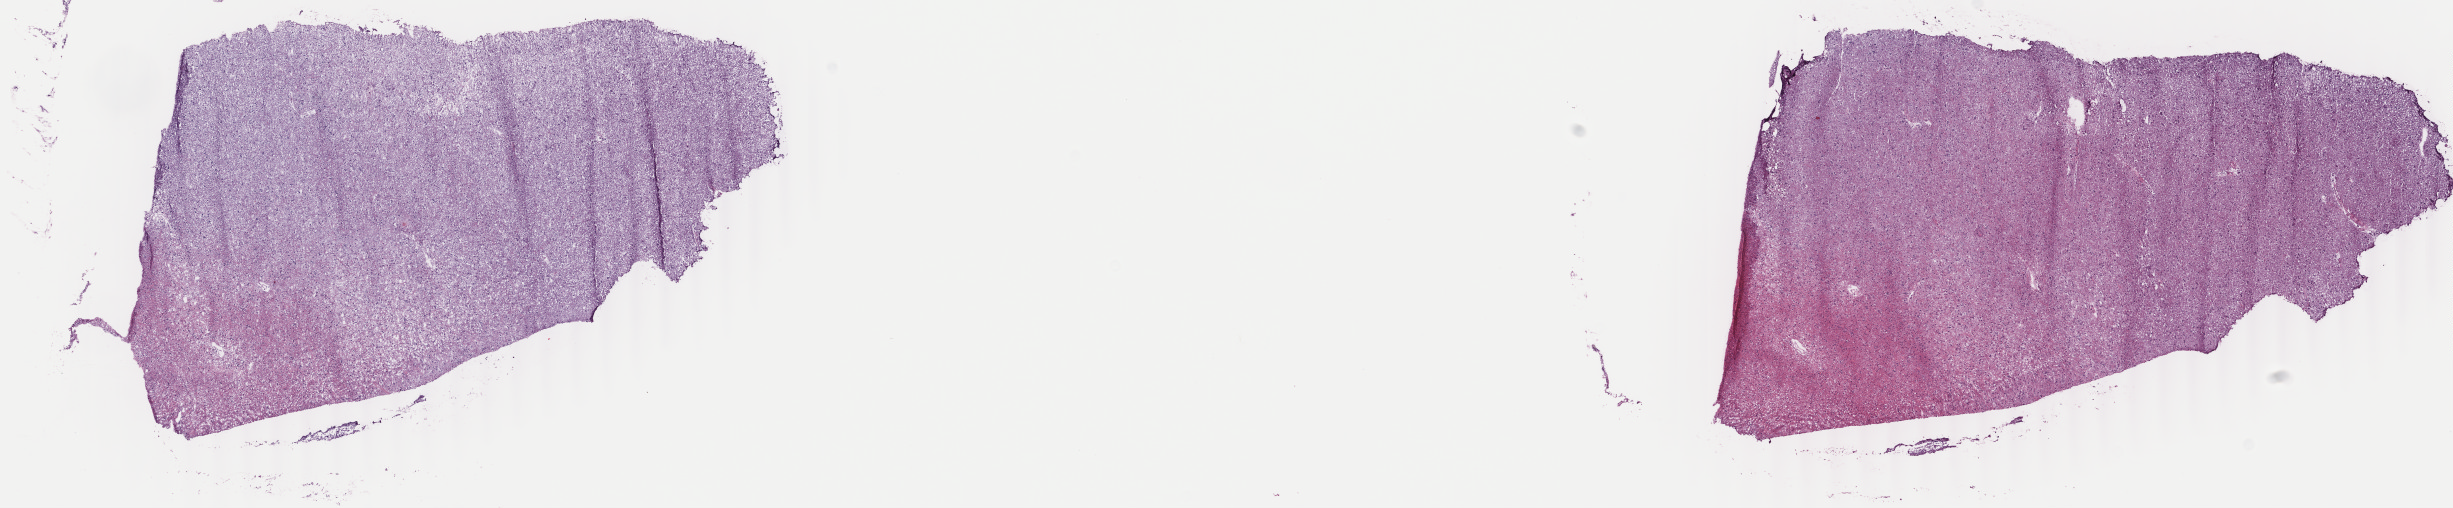
Digitized H&E-stained tissue section (whole slide), whole scanned area (about 19.5 x 4.0 mm, from a 40x scan) shown as a low-resolution overview, frozen section from the top of the tissue portion, sample: primary tumour, brain. Female, age 35 years at initial diagnosis. Histologic grade: G2 (moderately differentiated). Slide review estimates, as recorded: tumour cells 30%, tumour nuclei 80%, normal cells 10%, stromal cells 60%, necrosis 0%. Infiltration values recorded for this section: lymphocyte infiltration 0%, monocyte infiltration 0%, neutrophil infiltration 0%.
Histologic diagnosis: Mixed glioma (cerebrum). Laterality: left.